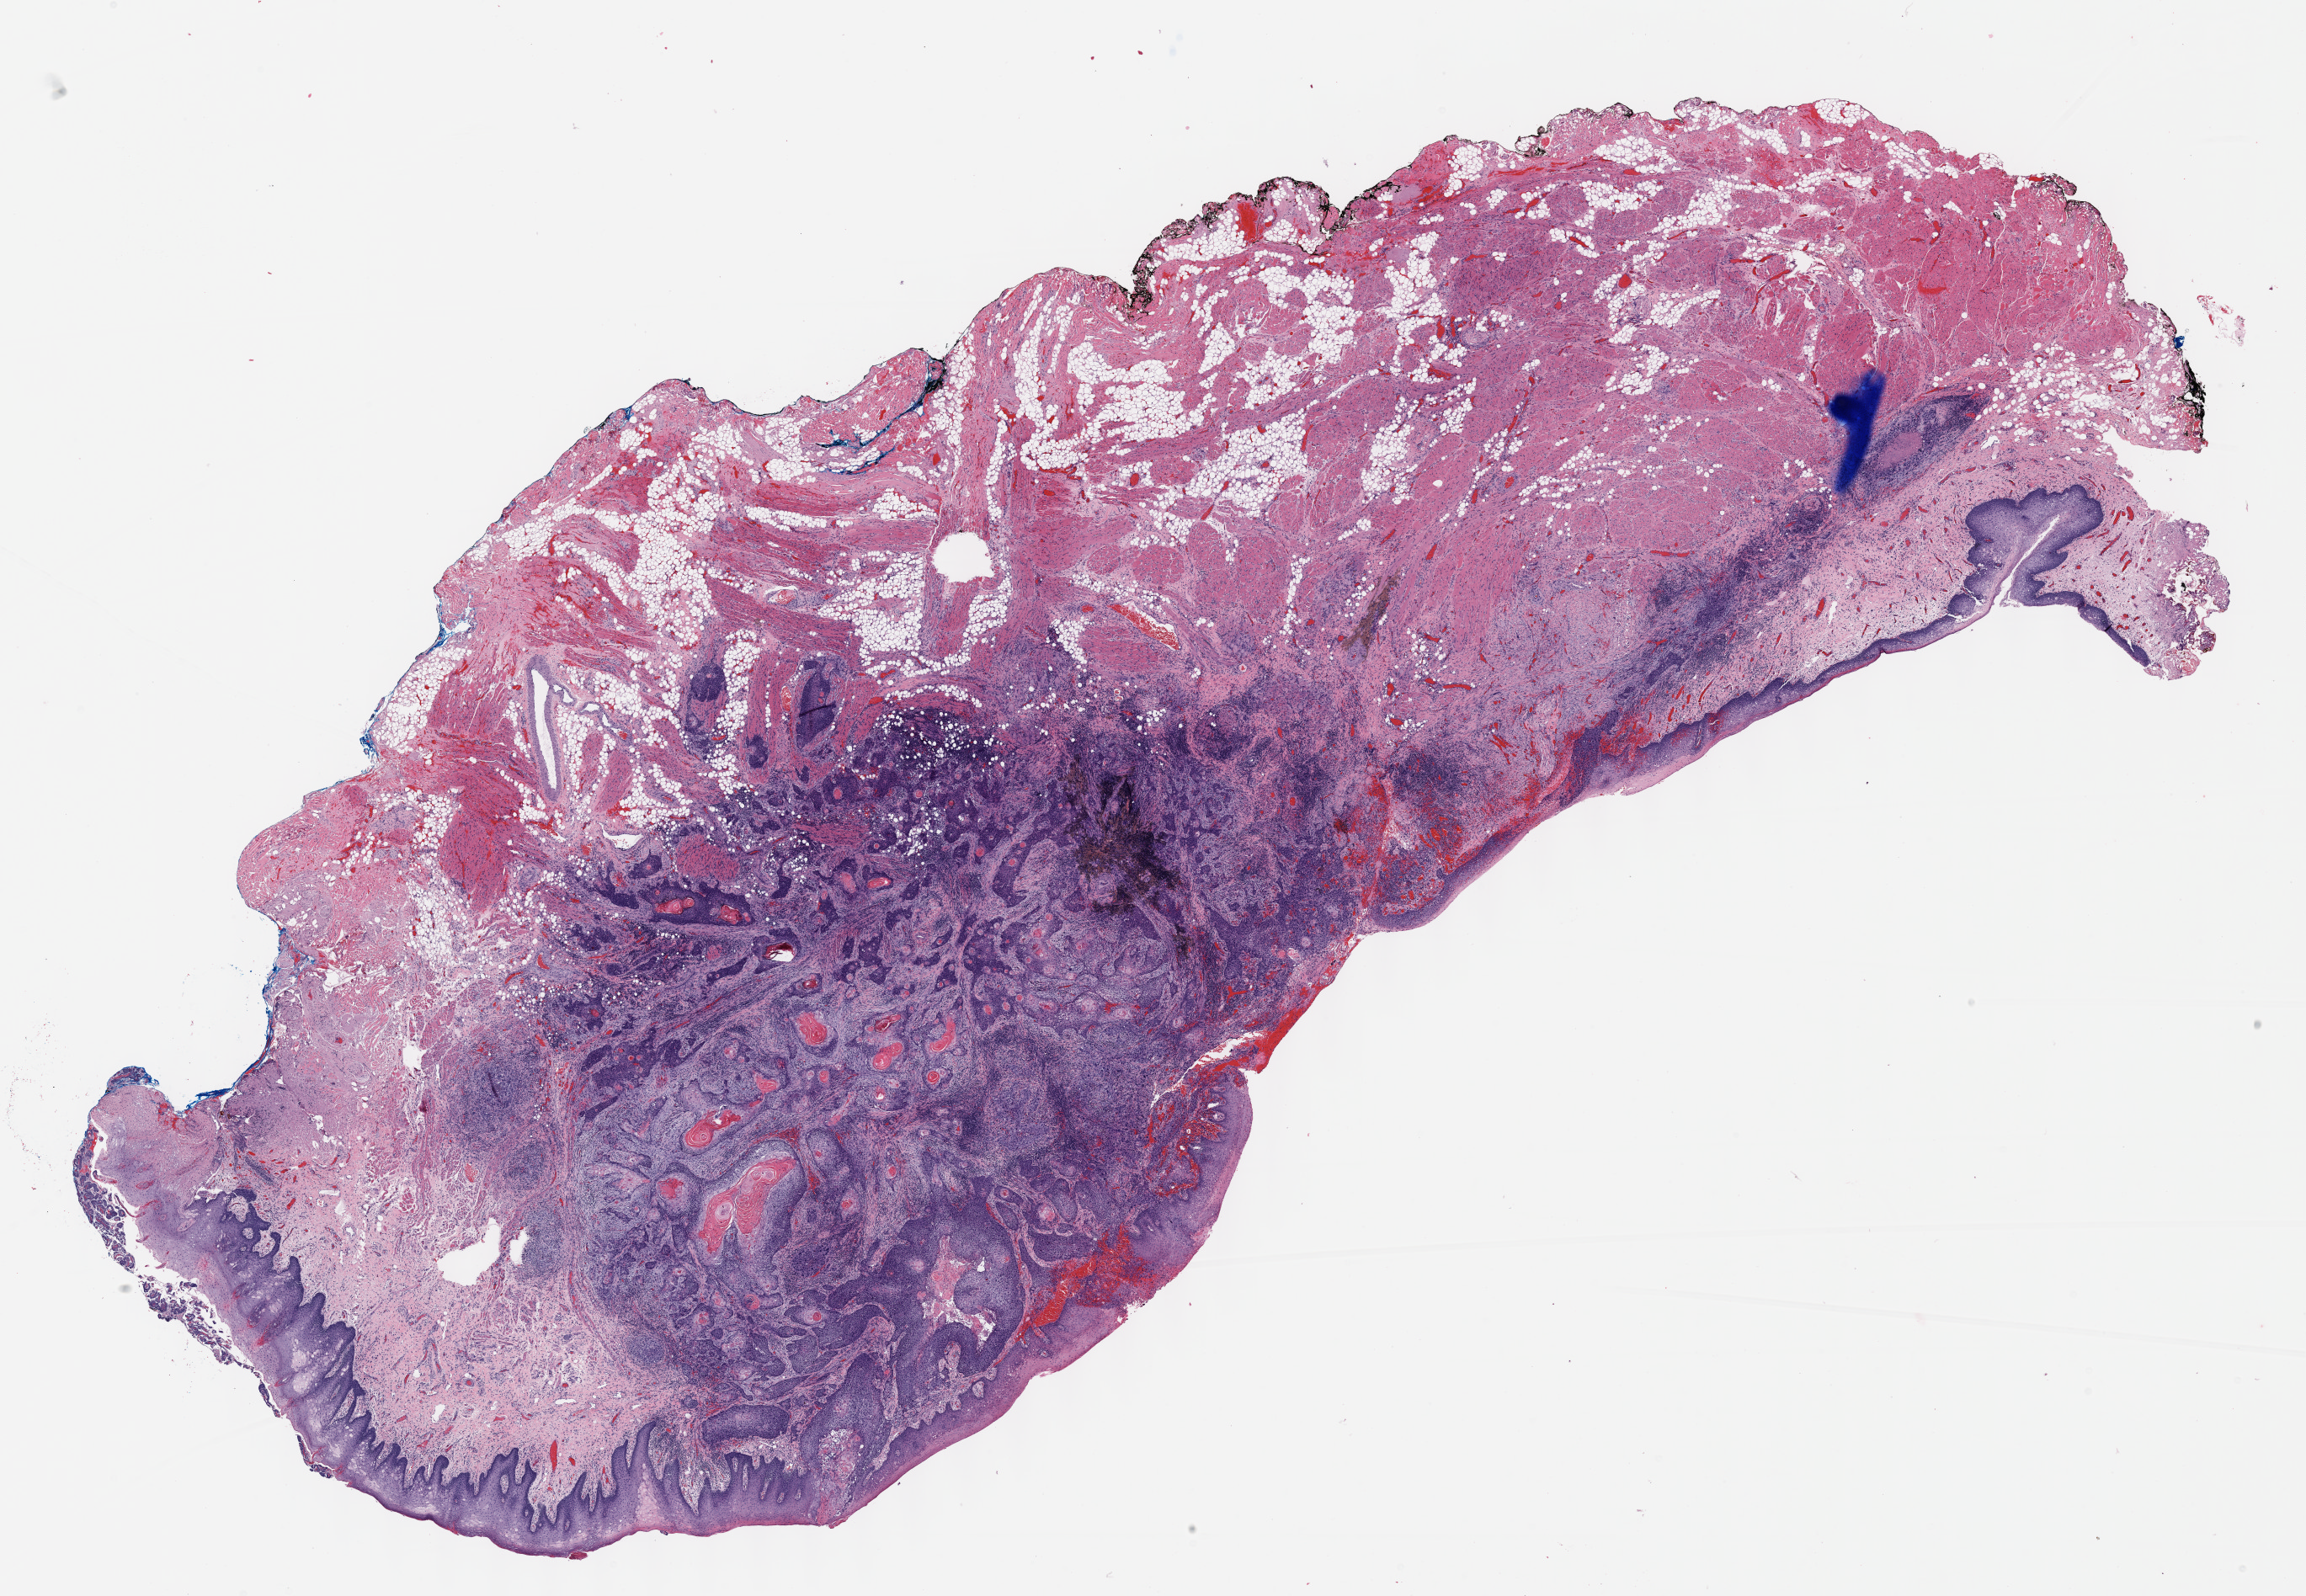
H&E-stained whole-slide image, low-resolution overview of the scanned area, about 22.1 x 15.3 mm (slide scanned at 40x); formalin-fixed paraffin-embedded (FFPE) diagnostic section; sample: primary tumour, head and neck. Male patient; age at initial diagnosis 41 years. Histologic grade: G3 (poorly differentiated).
AJCC pathologic stage: IVA (7th edition). Laterality: right. Pathologic diagnosis: Squamous cell carcinoma, NOS.